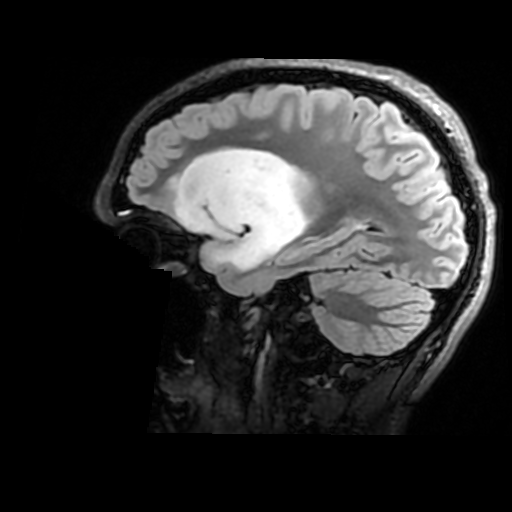
Brain MRI from a brain-tumour surgery series, one sagittal slice; position 116 of 176 along the scan axis; T2 FLAIR; 512 × 512 image matrix. Case-level facts recorded for this patient, not image findings: histopathology: Astrocytoma; WHO grade: 2; IDH mutation: yes; tumour location: Right Insular.
Outlined on this slice (manually delineated by an expert):
- tumour: bounding box (x1, y1, x2, y2) in pixels: (177, 147, 314, 273)